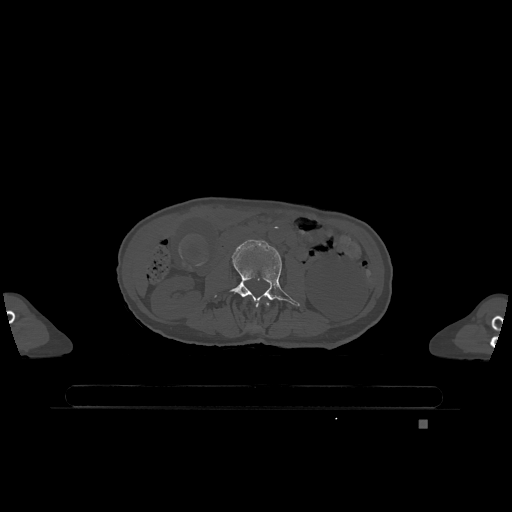
CT including the spine, one axial slice. Position 360 of 1317 along the scan axis. Bone window (W 1800 / L 400 HU). 0.5 mm slice thickness. 512 × 512 image matrix. Patient: female, 74 years. Case-level facts recorded for this patient, not image findings: primary cancer: lung; vertebrae with lytic lesions (as recorded): T1, T4, T5, T6, L4, L5.
Outlined on this slice (semi-automatically segmented with operator editing):
- L2 vertebra: bounding box <266,301,270,306> (left, top, right, bottom; pixels)
- L3 vertebra: <214,240,300,307>